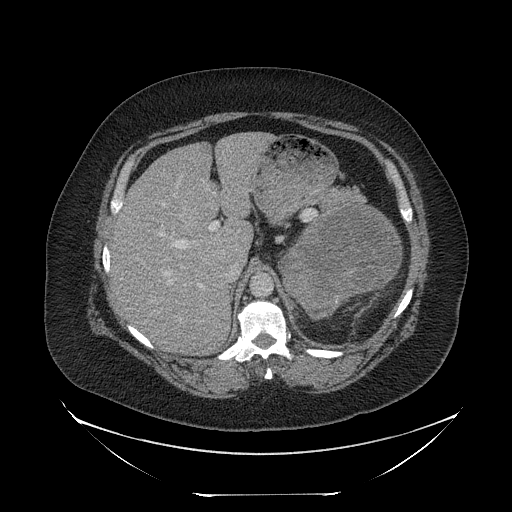
Contrast-enhanced abdominal CT, one axial slice; slice 159 of 205 in the series (ordered by position); intravenous contrast given; soft-tissue window (W 400 / L 40 HU); 2.5 mm slice thickness; 512 × 512 image matrix, field of view 500 × 500 mm. Female patient, age 53 years. From the clinical record (not read from this slice): diagnosis: adrenocortical carcinoma; tumour side: left adrenal; tumour size at pathology: 17 cm; Ki-67 index: 20 %; stage (as recorded): 3.
Annotated regions visible in this slice (semi-automatic segmentation, software-assisted and operator-edited):
- mass: box from (x=281, y=205) to (x=400, y=317) px